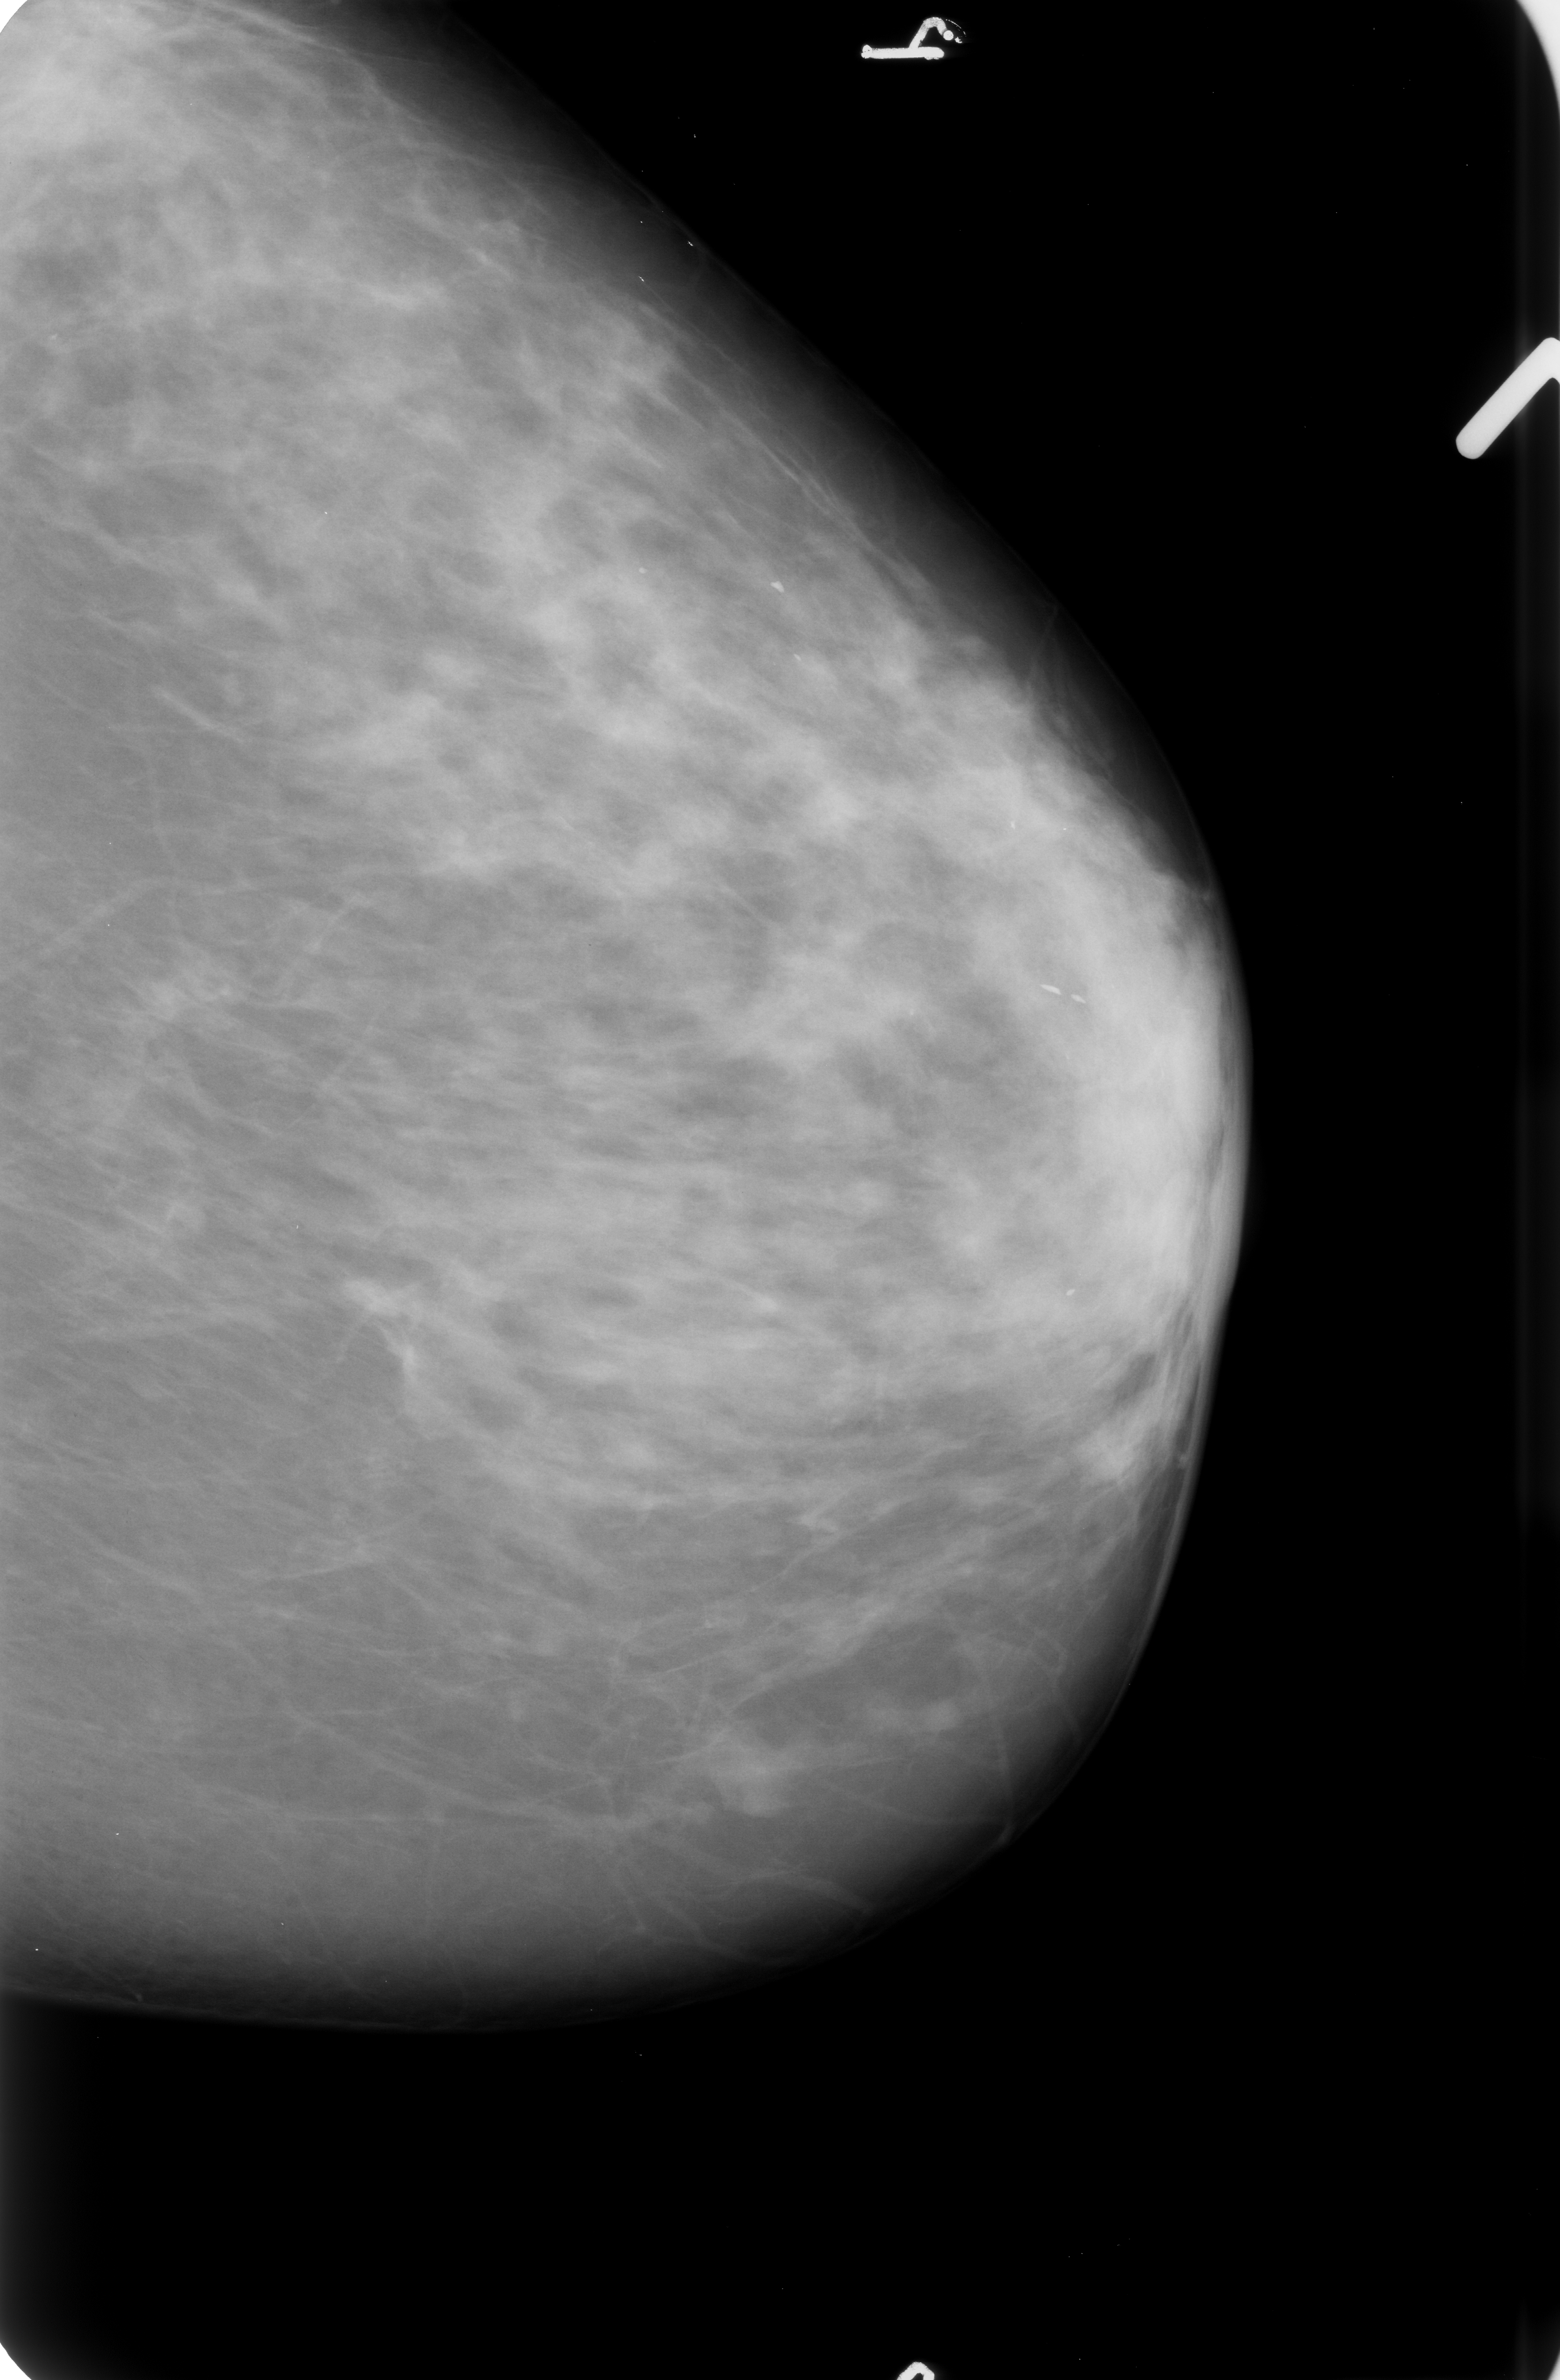
Scanned film-screen mammogram; left breast; CC view; BI-RADS breast density category 3 (scale 1–4).
Radiologist-marked abnormalities on this image: Finding 1 of 3: calcifications, morphology vascular / coarse; BI-RADS assessment category 2; subtlety rating 3 on a 1 (subtle) to 5 (obvious) scale; benign without callback (not worked up further). Finding 2 of 3: calcifications, morphology vascular / coarse; BI-RADS assessment category 2; subtlety rating 3 on a 1 (subtle) to 5 (obvious) scale; benign; no additional work-up was recommended (benign without callback). Finding 3 of 3: calcifications, morphology vascular / coarse; BI-RADS assessment category 2; subtlety rating 3 on a 1 (subtle) to 5 (obvious) scale; benign without callback (not worked up further).